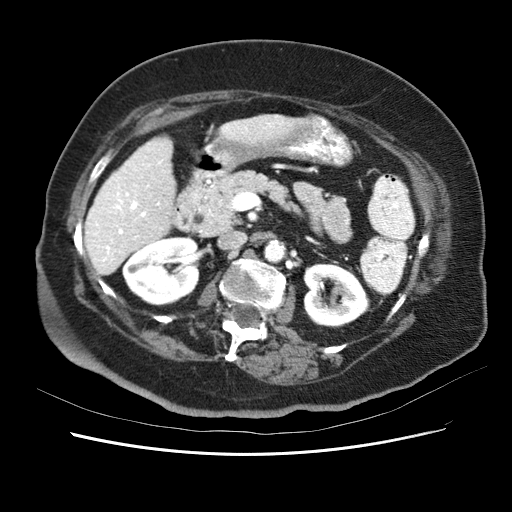
Contrast-enhanced abdominal CT (liver protocol), one axial slice; position 21 of 62 along the scan axis; soft-tissue window (W 400 / L 40 HU); 2.5 mm slice thickness; 512 × 512 image matrix. From the clinical record (not read from this slice): diagnosis: hepatocellular carcinoma (patient treated with transarterial chemoembolisation; whether this scan precedes or follows treatment is not stated here); TNM stage (as recorded): Stage-I.
Structures marked on this image (semi-automatically segmented with operator editing):
- liver parenchyma outside the tumour (the mass and vessels are separate outlines, so this box may not span the whole liver): box from (x=84, y=112) to (x=289, y=262) px
- liver vessels: (x=89, y=113)–(x=281, y=258)